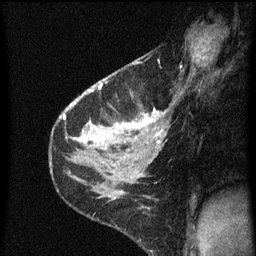
Breast MRI (dynamic contrast-enhanced), one sagittal slice. Slice 43 of 60 in the series (ordered by position). Dynamic contrast-enhanced series, image 2 of 3 at this slice position (ordered by acquisition). 1.5 T. TE 4.2 ms, TR 8 ms. 2 mm slice thickness. 256 × 256 image matrix. Patient: female, 38 years.
Outlined on this slice (semi-automatic segmentation, software-assisted and operator-edited):
- analysis volume of interest (the breast-tissue region the enhancement analysis was run in; not a lesion): box from (x=80, y=58) to (x=171, y=151) px
- tumour enhancement mask (voxels above the 70 % enhancement threshold inside the analysis volume of interest): (x=80, y=84)–(x=165, y=145)